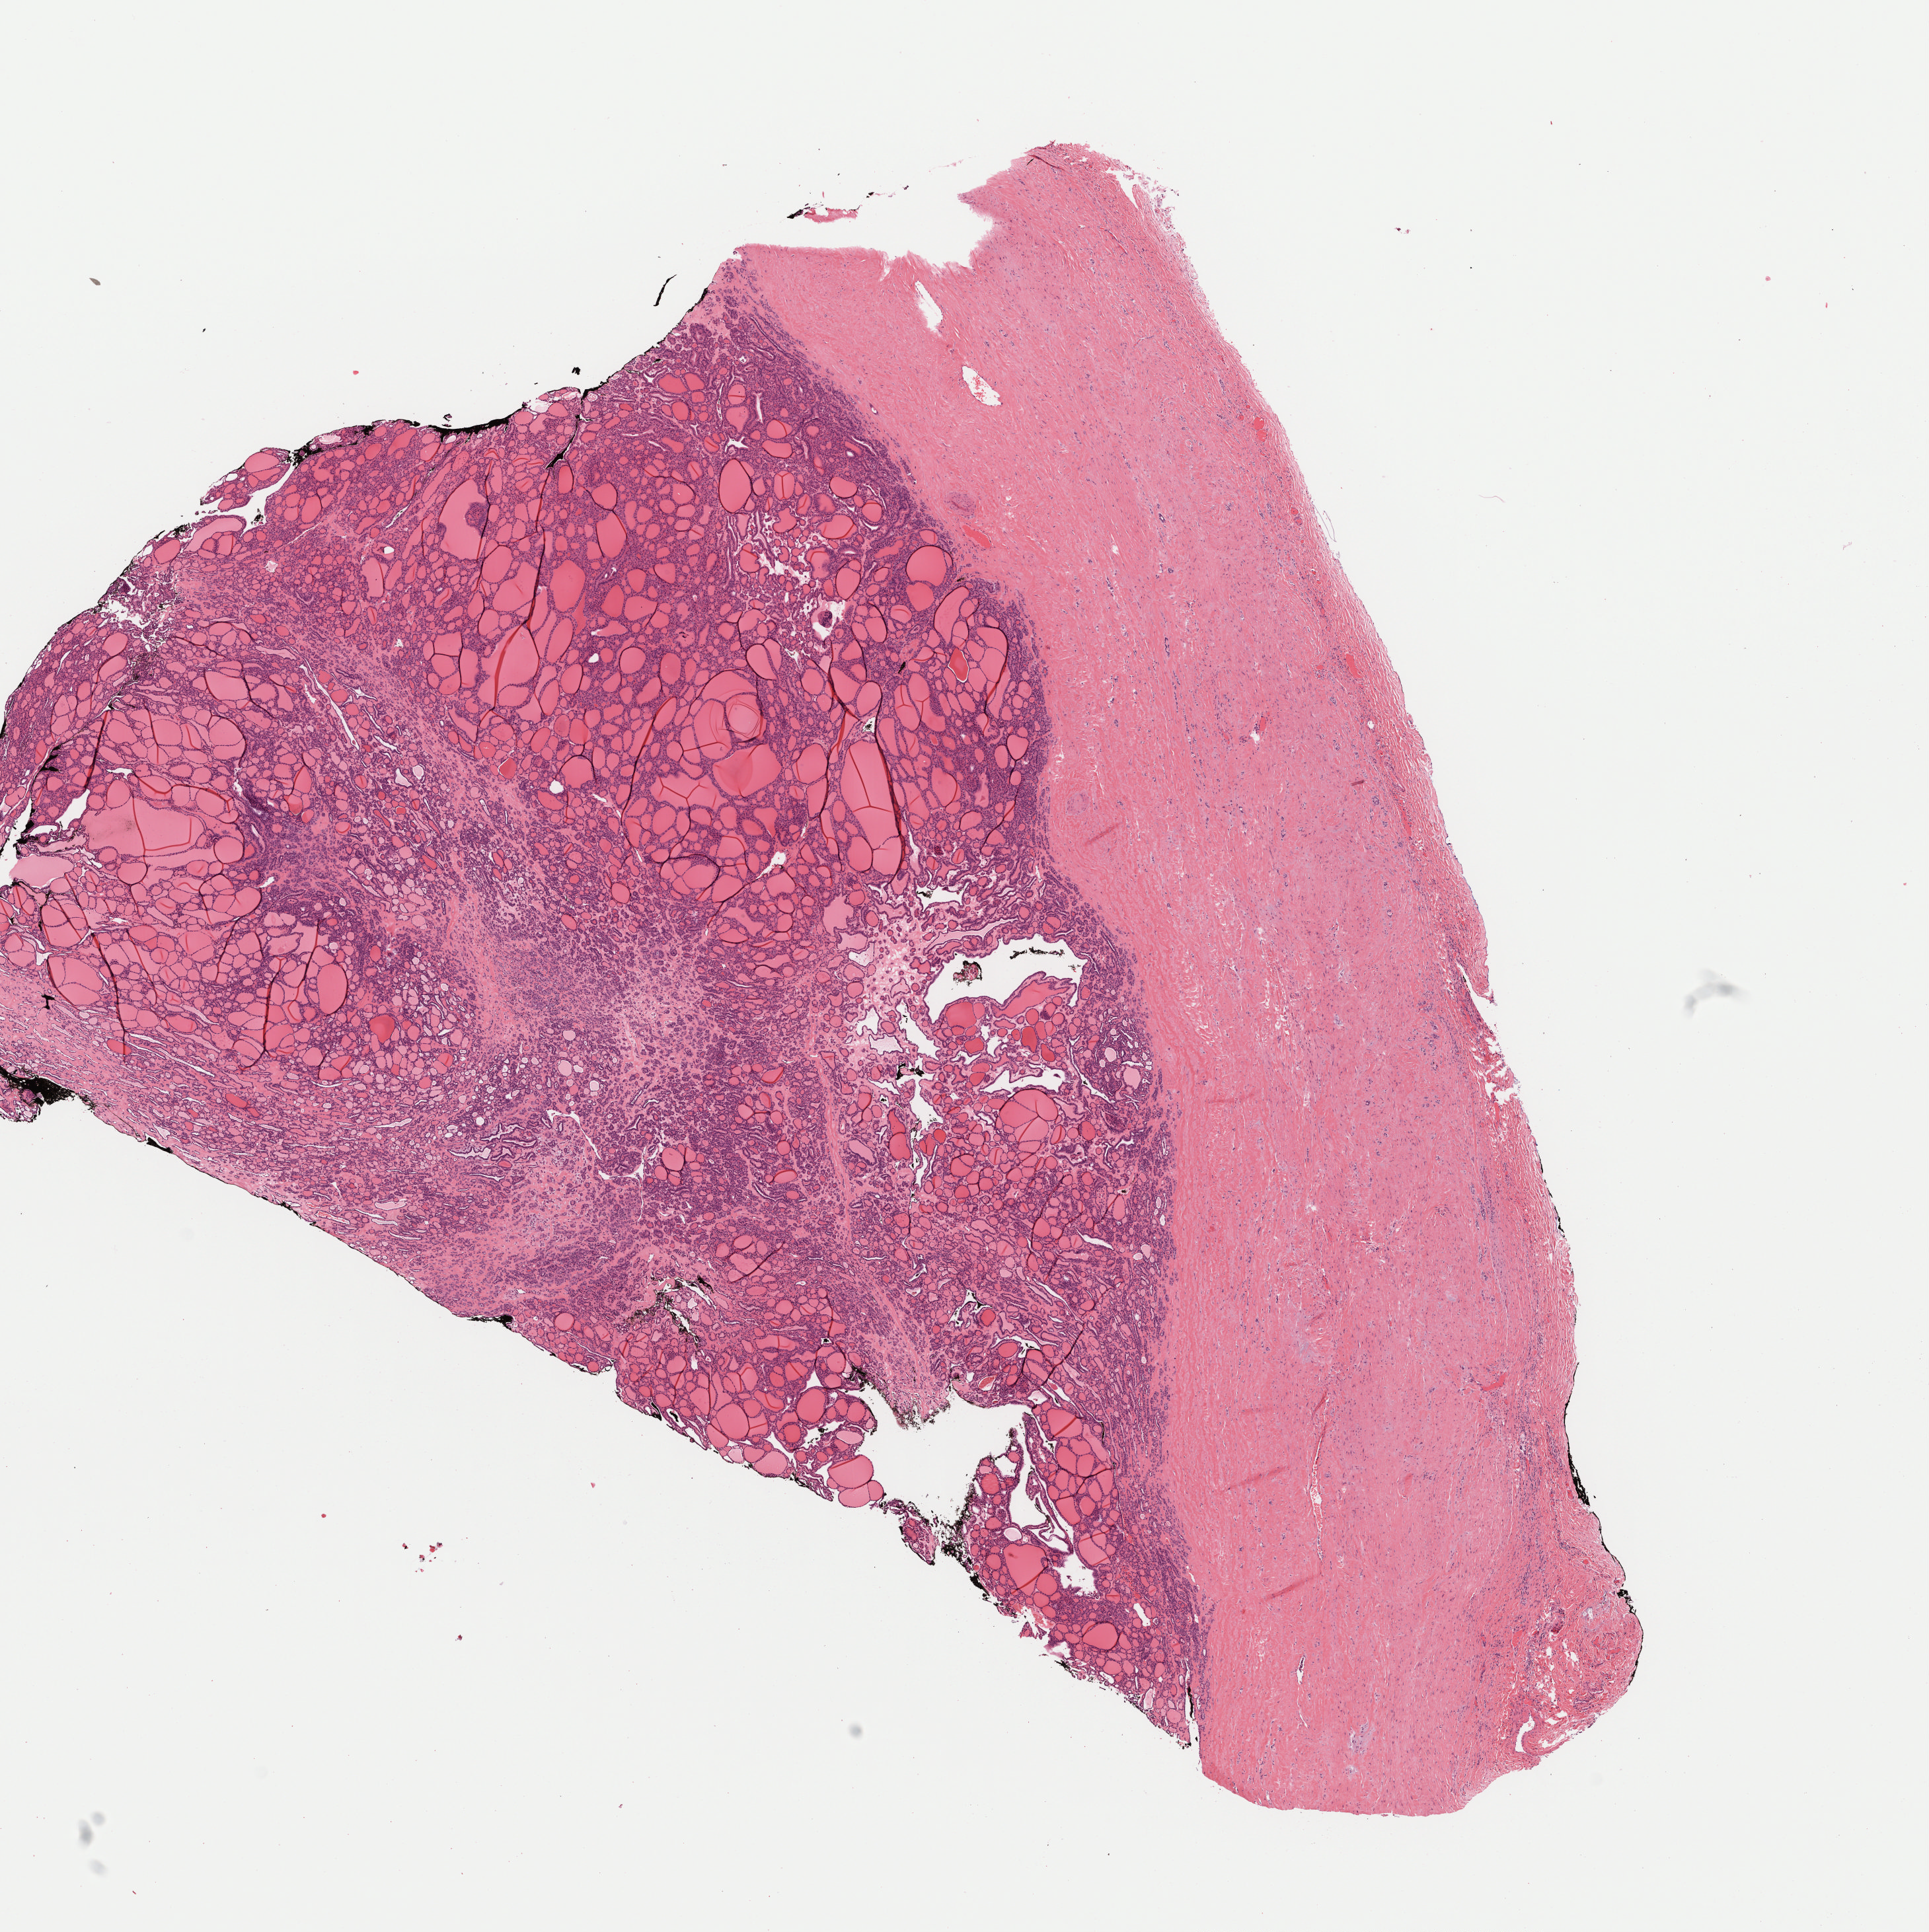
H&E-stained whole-slide image — shown as a low-resolution overview of the whole scanned area (about 11.8 x 11.8 mm); formalin-fixed paraffin-embedded (FFPE) diagnostic section; thyroid, primary tumour sample. Patient: female, age at initial diagnosis 26 years.
- AJCC pathologic stage: I (7th edition)
- laterality: left
- lymph nodes positive (case pathology): 0 of 2 examined
- diagnosis: Papillary carcinoma, follicular variant (thyroid gland)